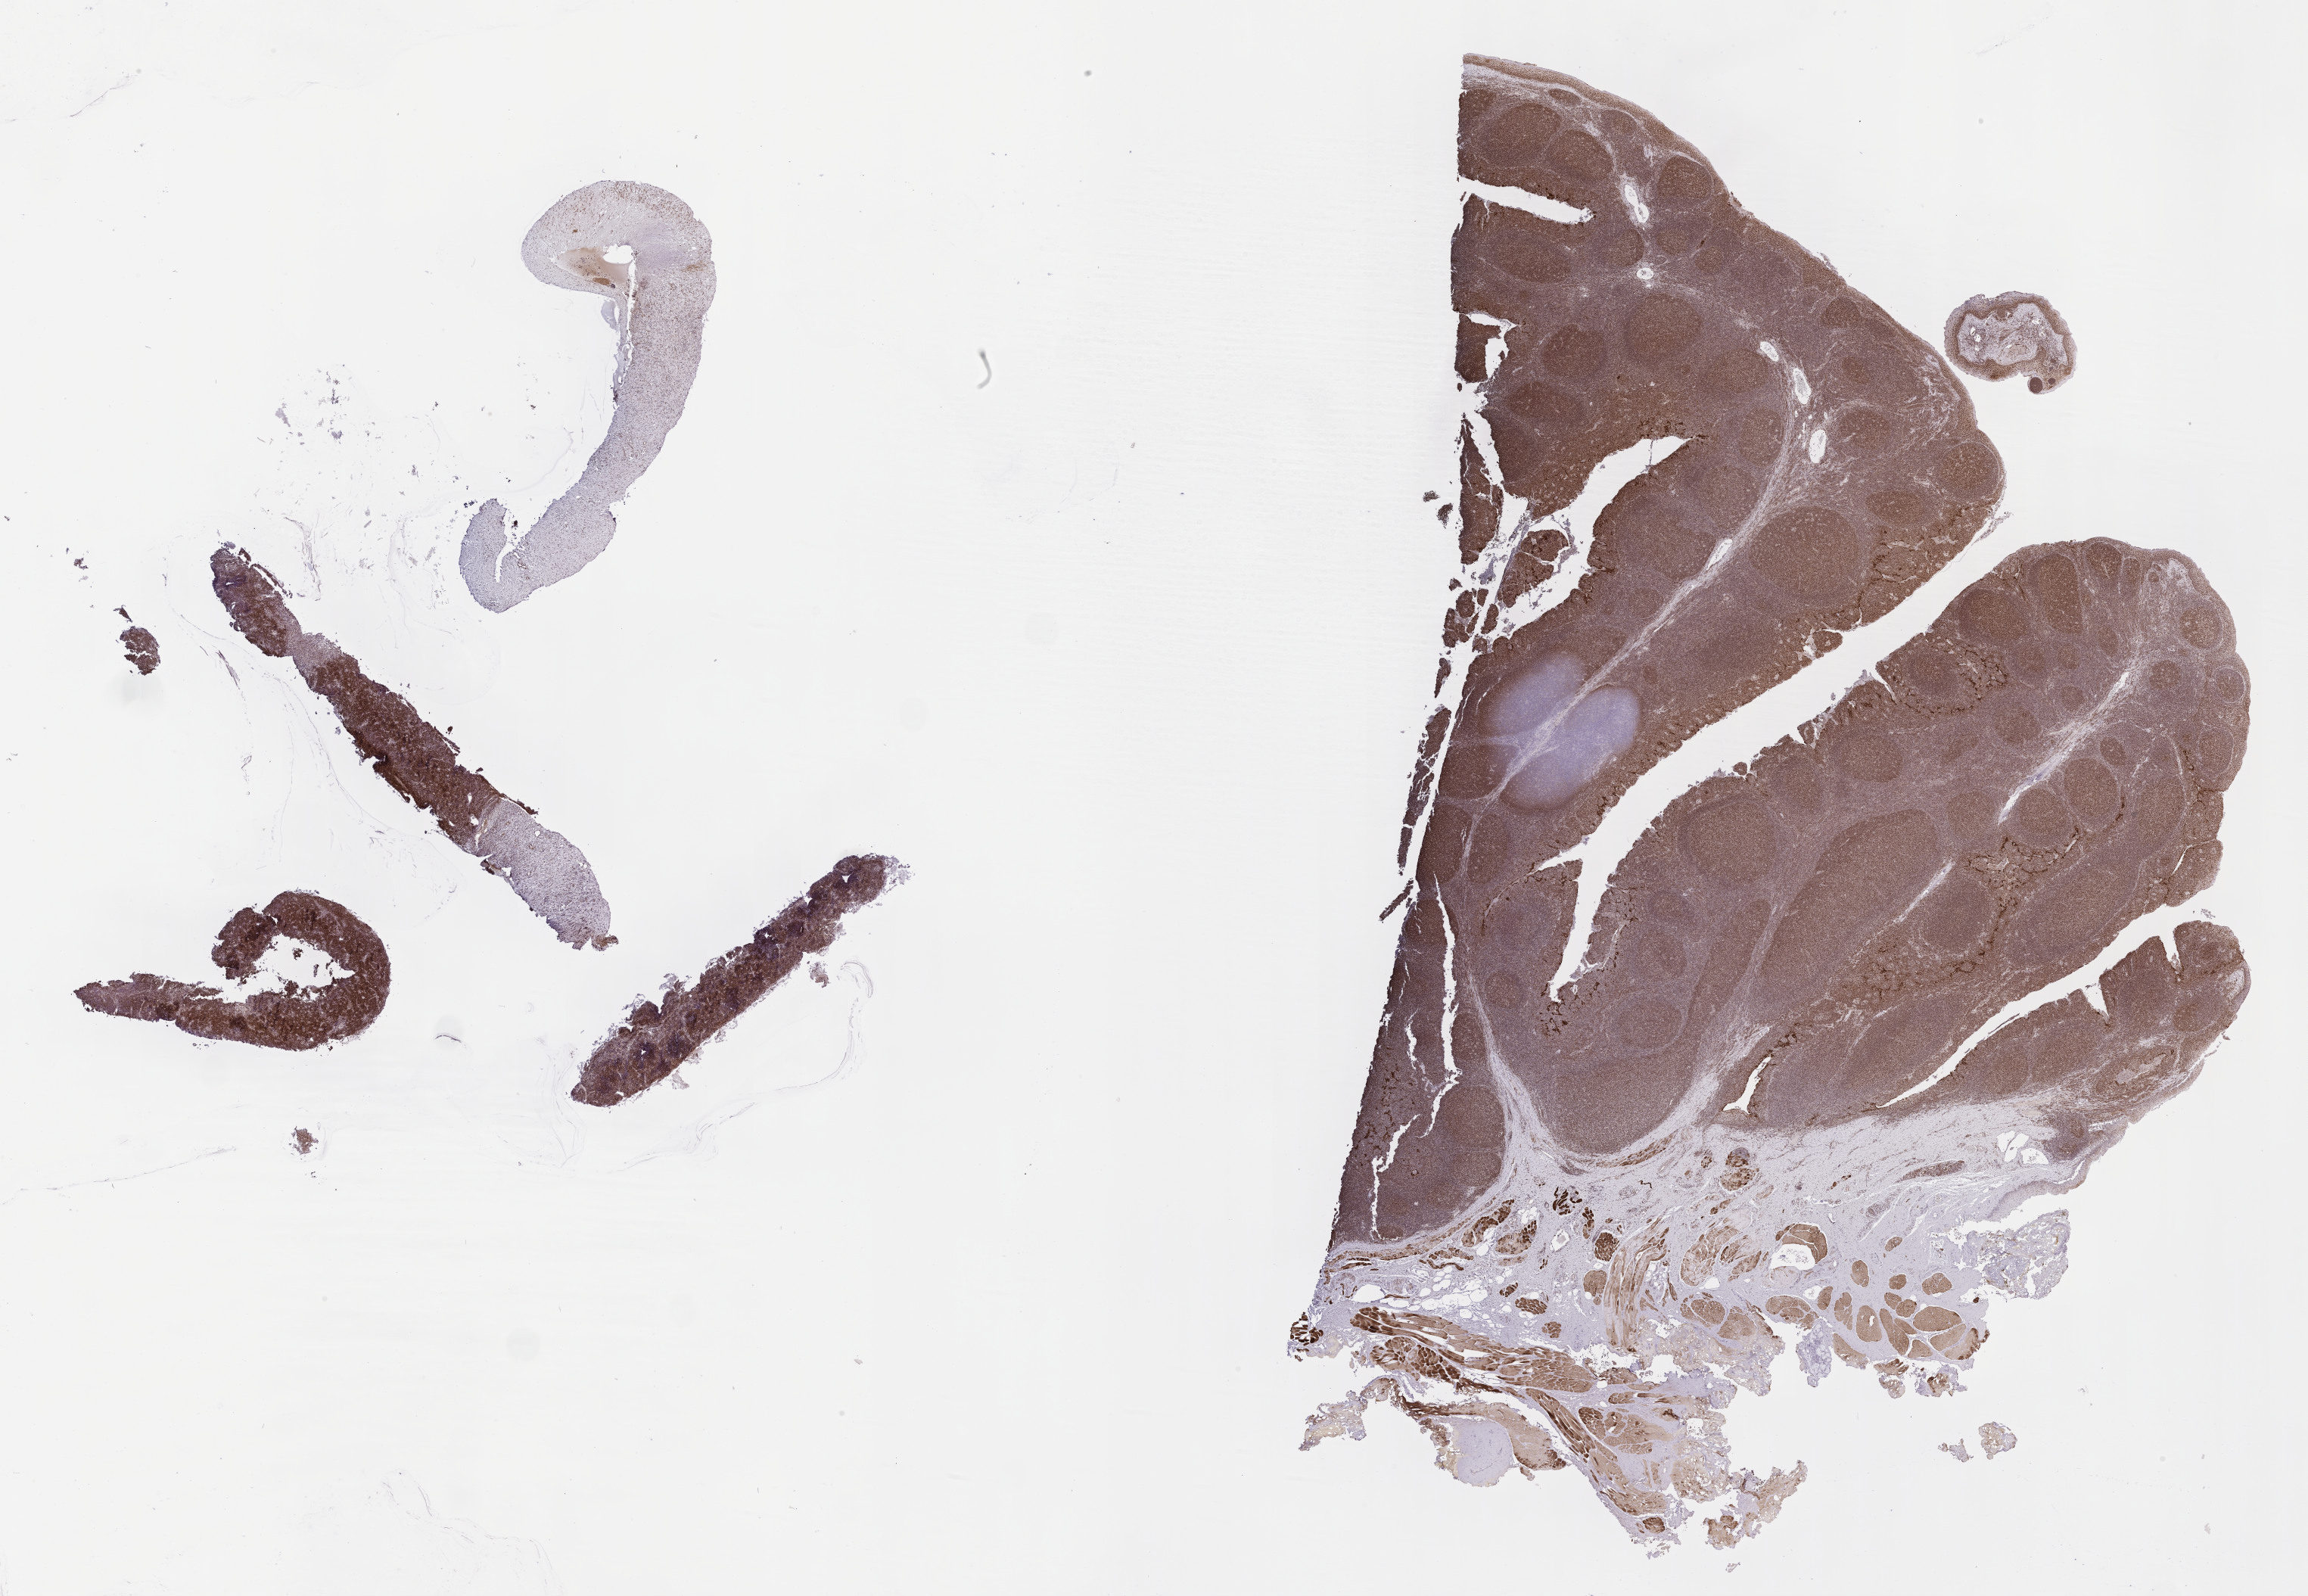
Whole-slide image, immunohistochemical stain for BCL6 — low-resolution overview of the scanned area, about 24.7 x 17.0 mm. Patient sex: male.
* specimen: tumor tissue